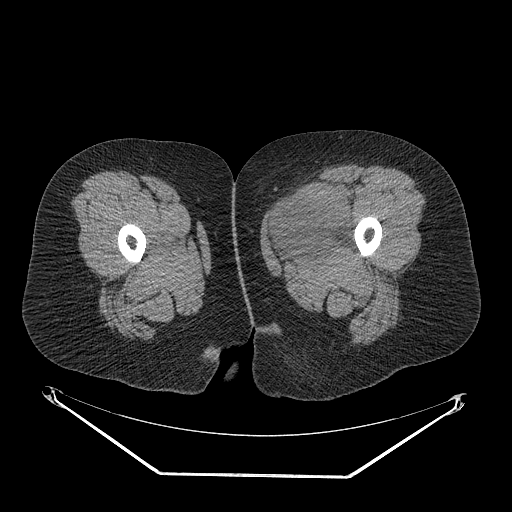
CT of an extremity soft-tissue mass (from a PET/CT study), one axial slice; slice 22 of 267 in the series (ordered by position); reconstruction kernel STANDARD; soft-tissue window (W 400 / L 40 HU); 3.75 mm slice thickness; 512 × 512 image matrix, field of view 500 × 500 mm. Female patient. From the clinical record (not read from this slice): histological type: myxofibrosarcoma; grade: intermediate; site of the primary tumour: left thigh.
Outlined on this slice (expert contour drawn on MRI and transferred to this co-registered scan by the dataset authors):
- gross tumour volume including surrounding oedema: bounding box [x1, y1, x2, y2] px = [269, 185, 355, 259]
- gross tumour volume (mass): [272, 190, 353, 255]